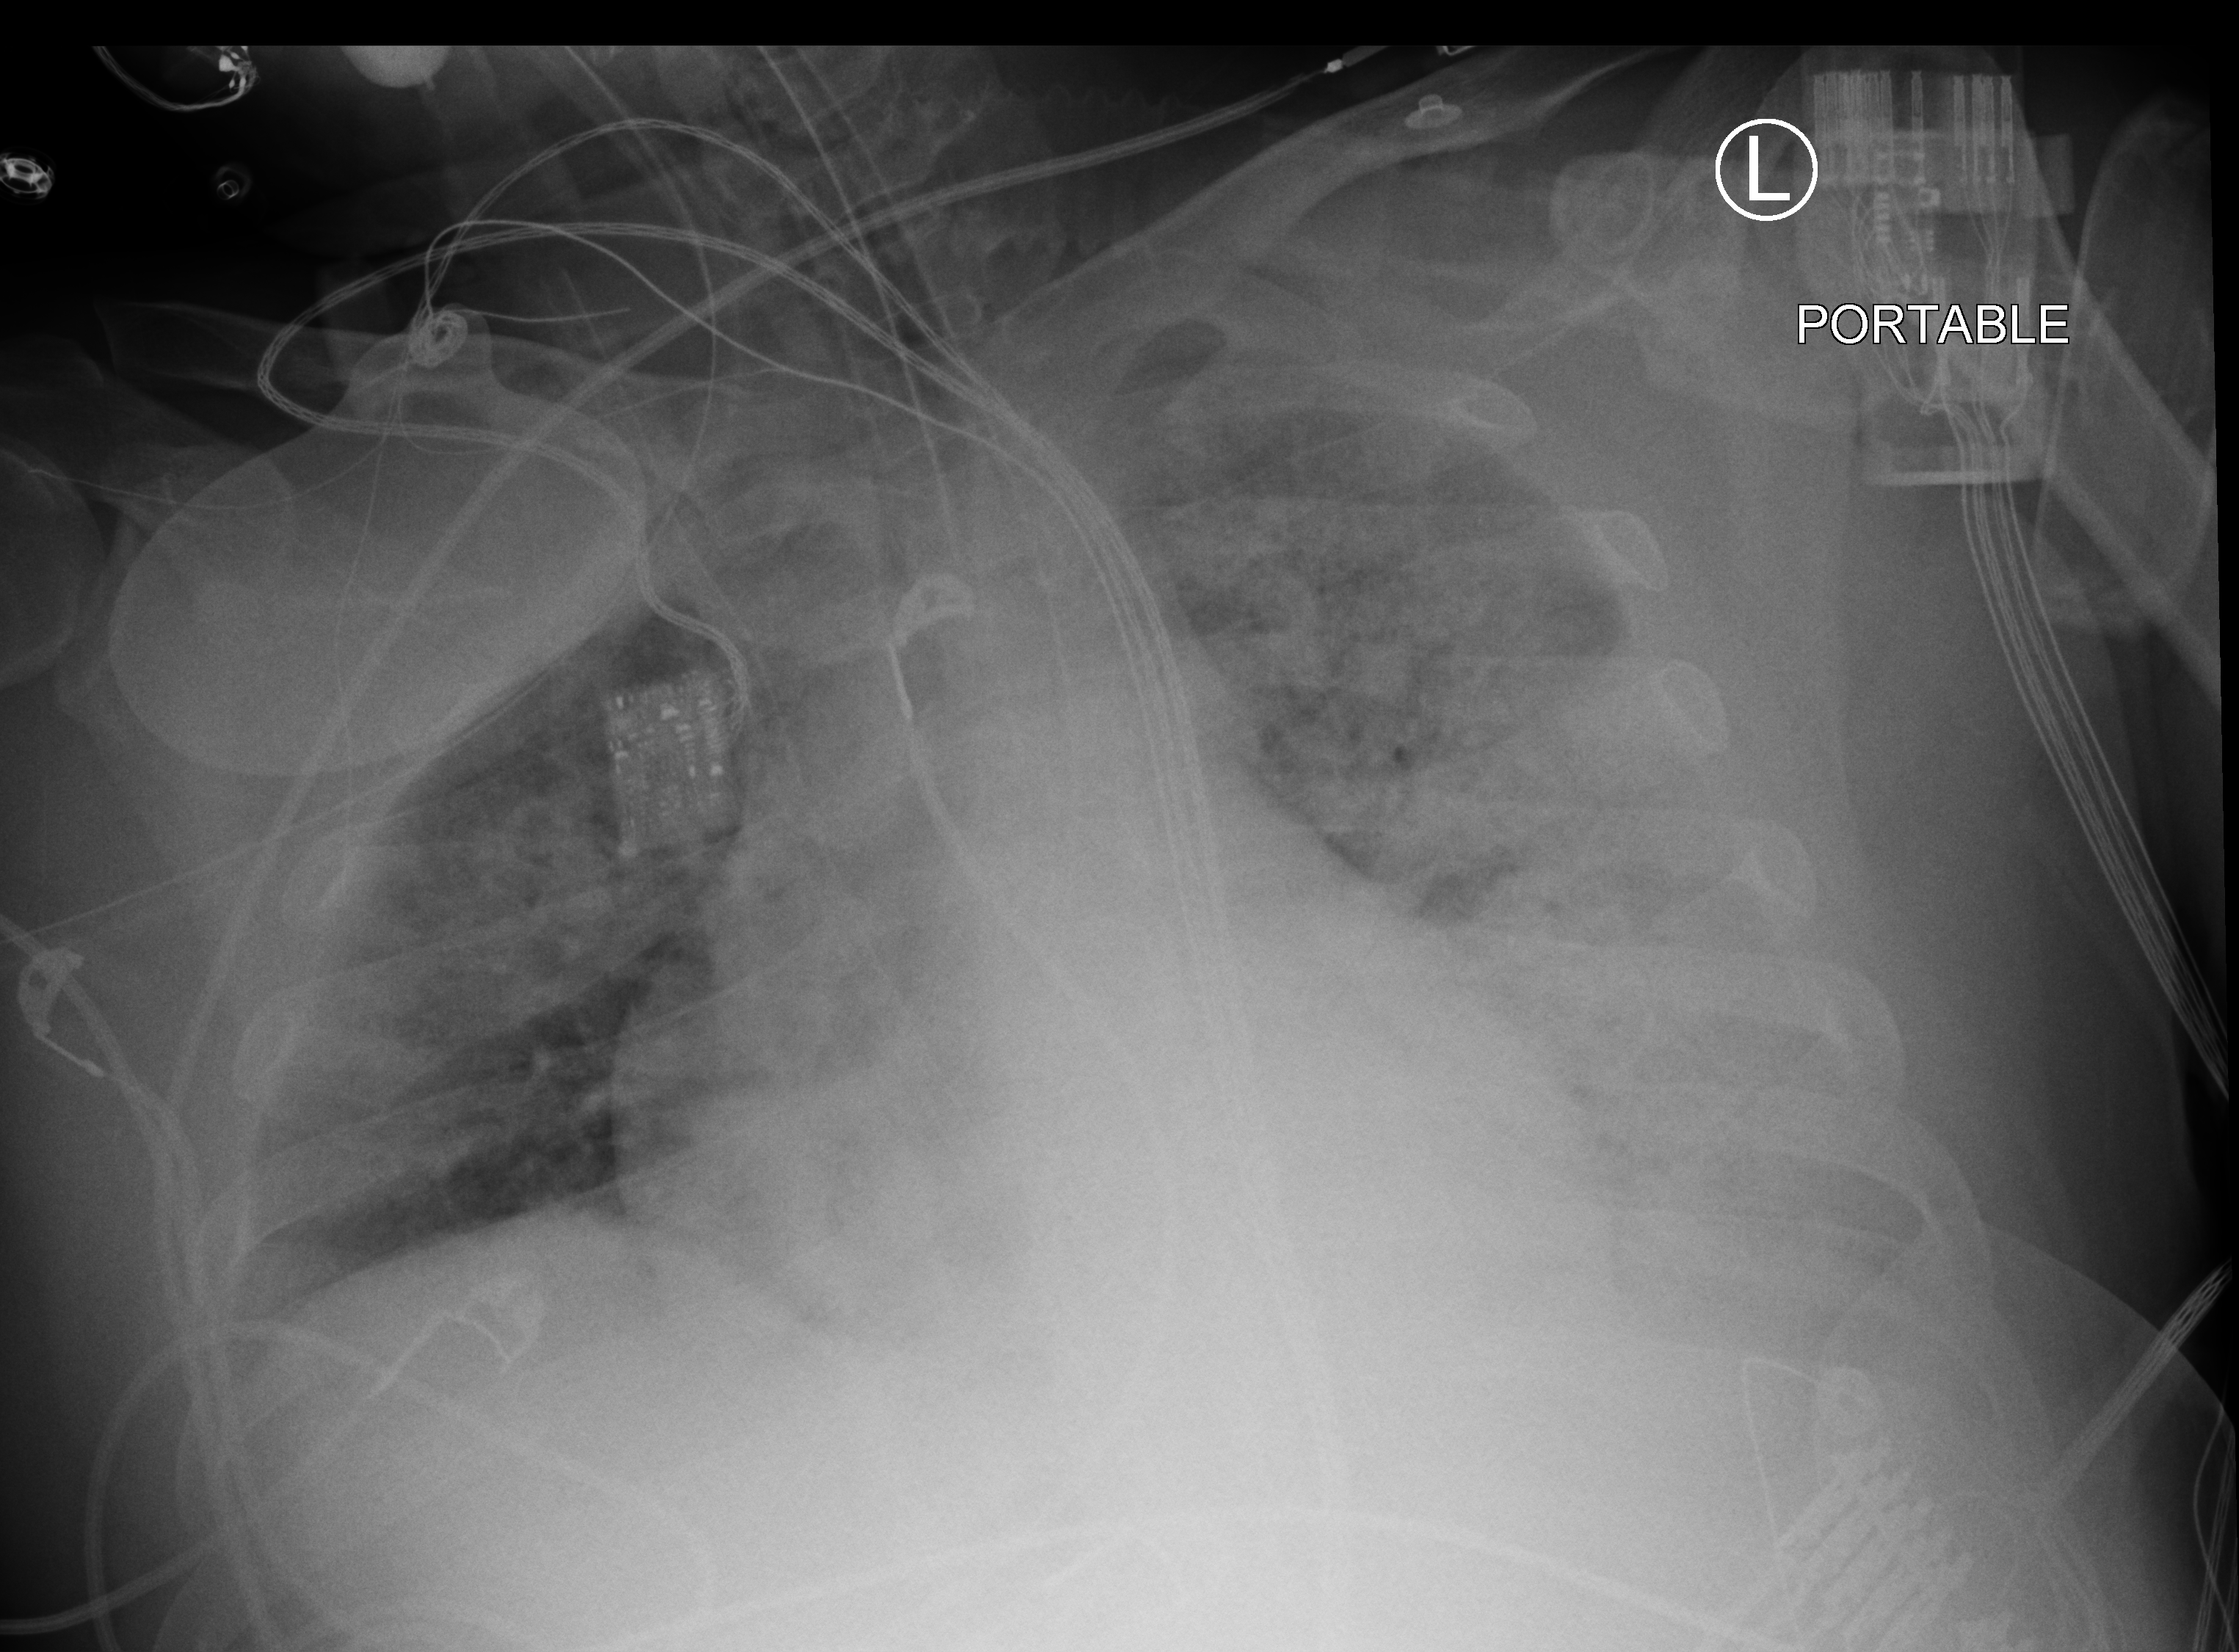
Bedside chest radiograph (computed radiography); anteroposterior (AP) projection. Patient hospitalised with COVID-19; male, aged 18–59 years.
Admission-level facts for this patient (not findings on this image; timing relative to this image not recorded):
- admitted to intensive care during this hospital stay: yes